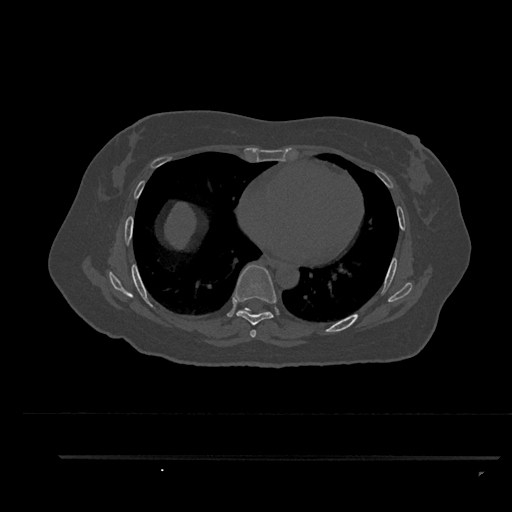
CT including the spine, one axial slice. Position 501 of 797 along the scan axis. Reconstruction kernel Br40s/3. 120 kVp. Bone window (W 1800 / L 400 HU). 0.5 mm slice thickness. 512 × 512 image matrix, field of view 408 × 408 mm. Female patient, age 44 years. Case-level facts recorded for this patient, not image findings: primary cancer: renal.
Annotated regions visible in this slice (semi-automatic segmentation, software-assisted and operator-edited):
- T6 vertebra: bounding box <251,330,256,338> (left, top, right, bottom; pixels)
- T7 vertebra: <232,264,276,337>
- T8 vertebra: <239,308,268,315>